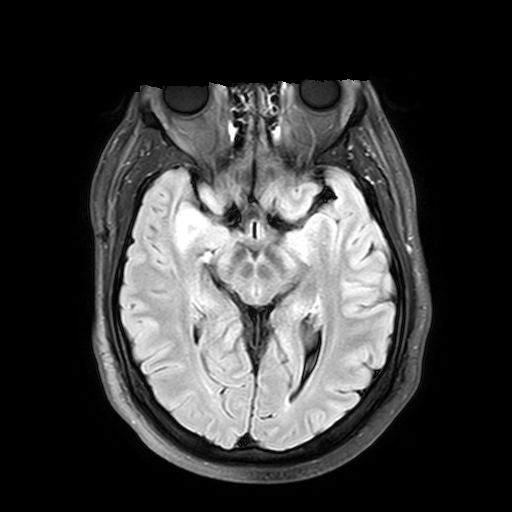
Brain MRI from a brain-tumour surgery series, one axial slice. Position 24 of 42 along the scan axis. T2 FLAIR. 4 mm slice thickness. 512 × 512 image matrix, field of view 240 × 240 mm. From the clinical record (not read from this slice): histopathology: Astrocytoma; WHO grade: 2; IDH mutation: yes.
Annotated regions visible in this slice (expert manual segmentation):
- tumour: bounding box [x1, y1, x2, y2] px = [137, 202, 223, 246]